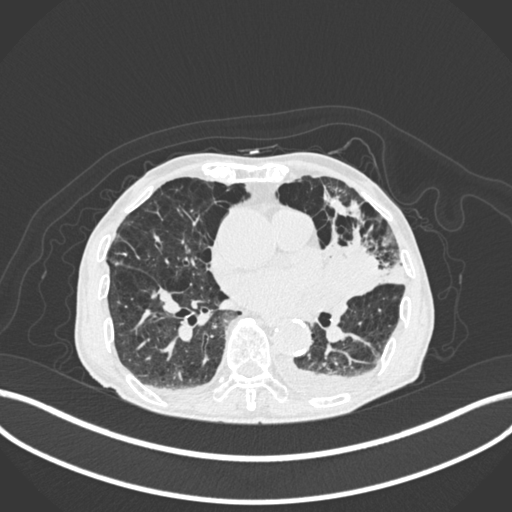
Chest CT, one axial slice; position 96 of 400 along the scan axis; reconstruction kernel B30f; lung window (W 1500 / L -600 HU); 1 mm slice thickness; 512 × 512 image matrix, field of view 400 × 400 mm. Patient: male, 90 years or older. From the clinical record (not read from this slice): clinical TNM (as recorded): T2b N1 M0.
Structures marked on this image (rectangle marked by the reading radiologist):
- lung tumour (recorded histology: squamous cell carcinoma): bounding box [x1, y1, x2, y2] px = [323, 238, 387, 303]